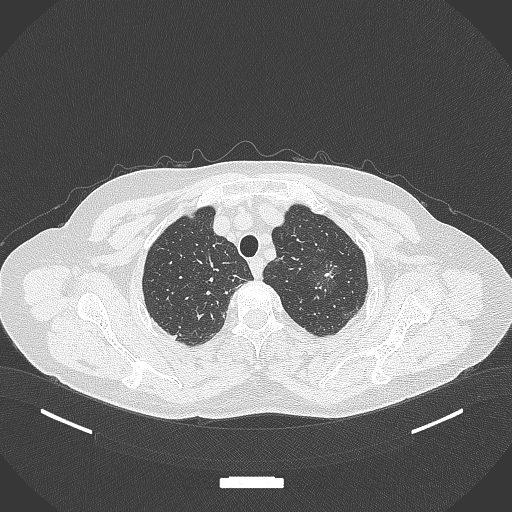
Chest CT, one axial slice; slice 306 of 369 in the series (ordered by position); 120 kVp; lung window (W 1500 / L -600 HU); 1 mm slice thickness; 512 × 512 image matrix. Female patient, age 64 years. From the clinical record (not read from this slice): clinical TNM (as recorded): T1c N0 M0.
Annotated regions visible in this slice (bounding box drawn by a radiologist):
- lung tumour (recorded histology: adenocarcinoma): bounding box <308,258,344,300> (left, top, right, bottom; pixels)